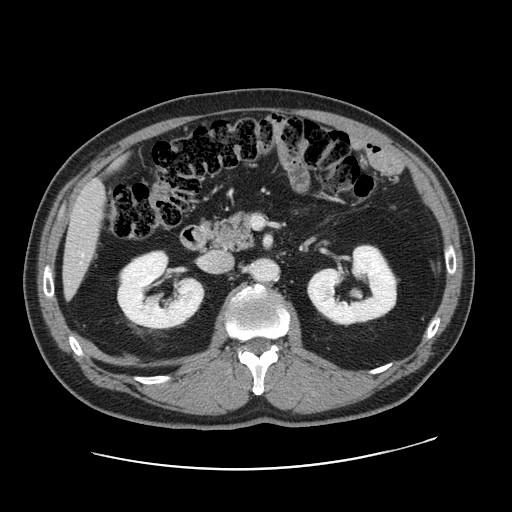
Contrast-enhanced abdominal CT, one axial slice; position 76 of 178 along the scan axis; 120 kVp; intravenous contrast given; soft-tissue window (W 400 / L 40 HU); 2.5 mm slice thickness; 512 × 512 image matrix, field of view 403 × 403 mm. Male patient, age 63 years. Case-level facts recorded for this patient, not image findings: diagnosis: colorectal cancer liver metastases, imaged before liver resection; multiple liver metastases: yes; largest metastasis: 8 cm; disease in both lobes: yes.
Outlined on this slice (expert manual segmentation):
- liver: bounding box [x1, y1, x2, y2] px = [63, 179, 105, 294]